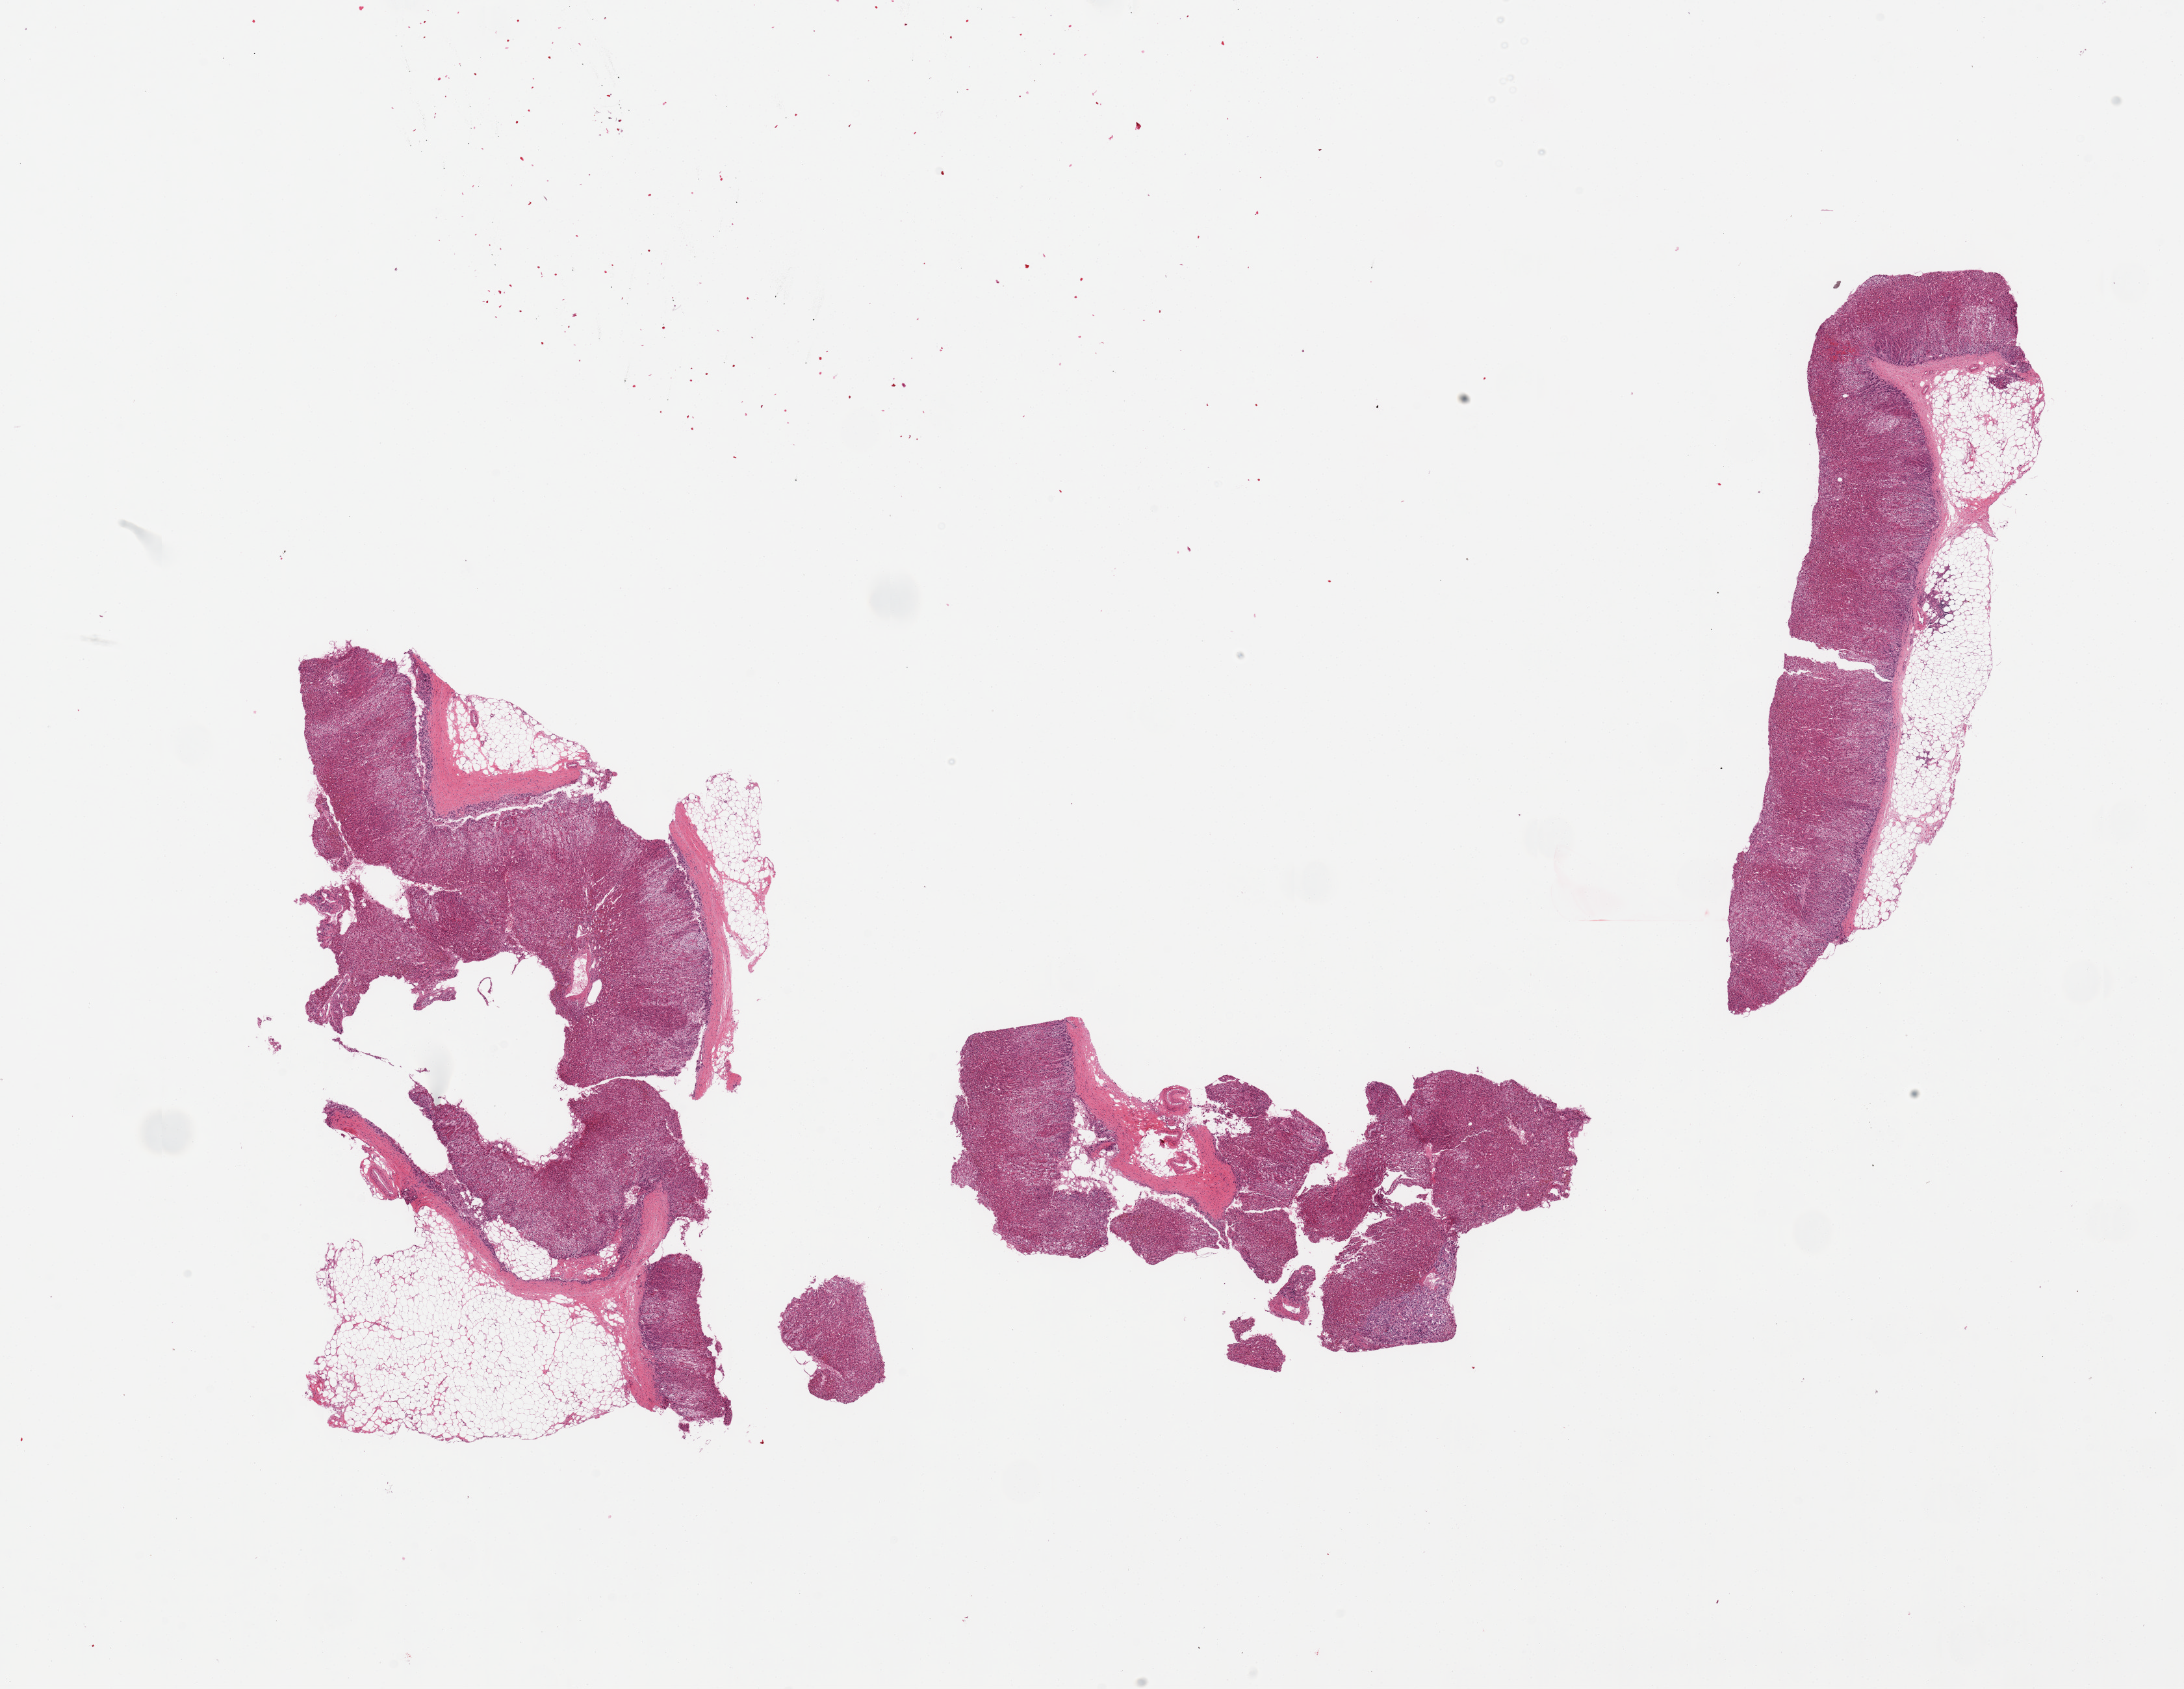
Whole-slide image, haematoxylin and eosin stain, brightfield — a low-resolution overview of the entire scanned area, about 26.6 x 20.6 mm. PAXgene-fixed, paraffin-embedded tissue. Target tissue: adrenal gland. Donor tissue sample. Donor: male.
Pathologist's review note for this sample: 3 fragmented pieces; up to 2.5mm external fat on 2 of the 3 pieces.